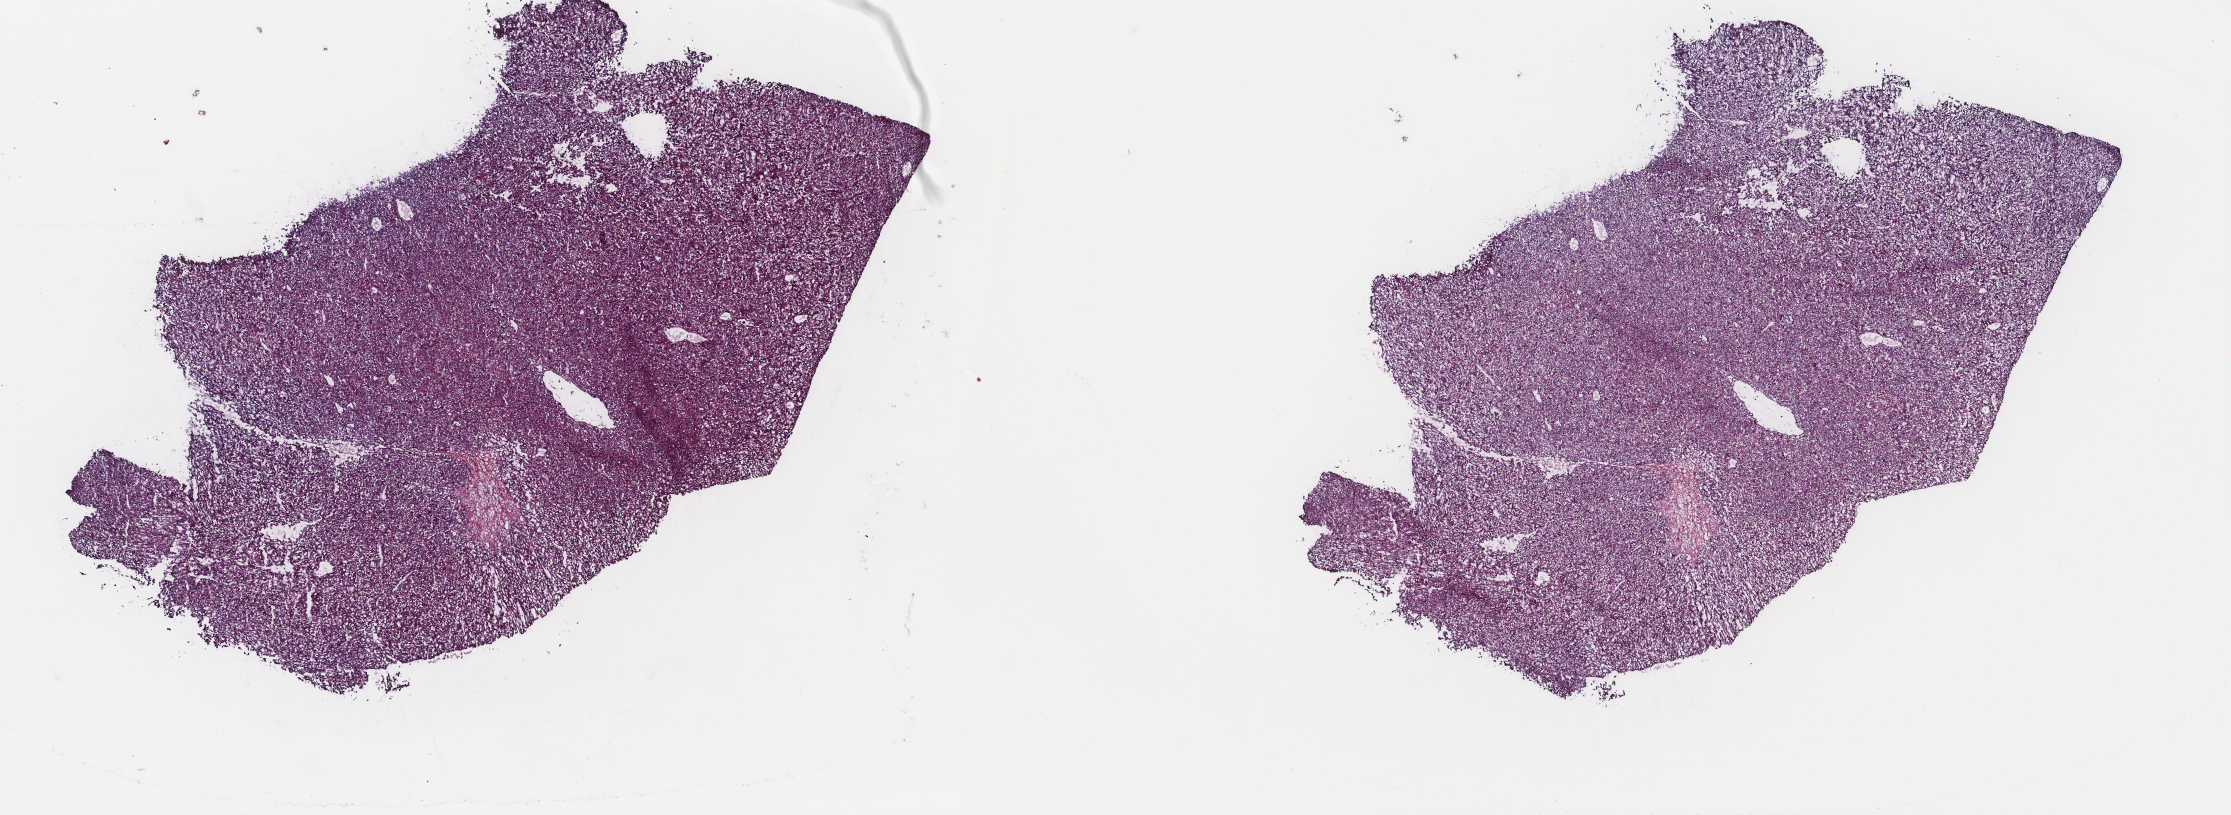
Hematoxylin and eosin (H&E) stained whole-slide image — shown as a low-resolution overview of the whole scanned area (about 17.7 x 6.5 mm, slide scanned at 40x), frozen section from the top of the tissue portion, primary tumour sample from the liver. Male, age 45 years at initial diagnosis. Histologic grade: G2 (moderately differentiated). Composition of this section per pathologist review: tumour cells 89%, tumour nuclei 95%, normal cells 0%, stromal cells 10%, necrosis 1%. Inflammatory infiltration, as recorded: lymphocyte infiltration 2%, monocyte infiltration 0%, neutrophil infiltration 0%.
* AJCC pathologic stage: IIIA (6th edition)
* pathologic diagnosis: Hepatocellular carcinoma, NOS